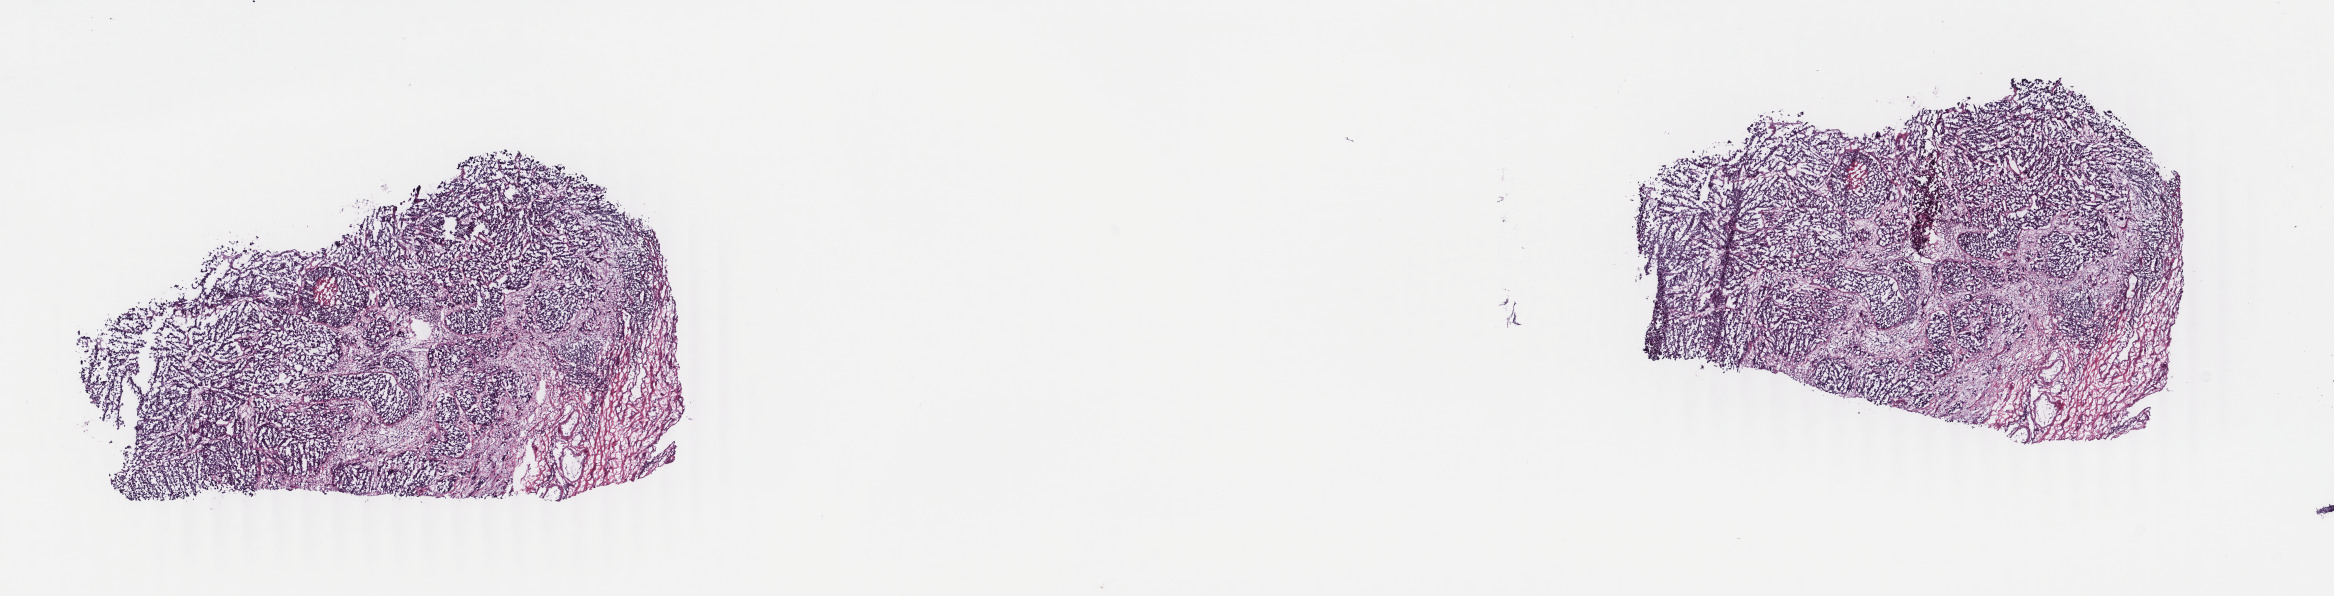
Digitized H&E-stained tissue section (whole slide), shown as a low-resolution overview of the whole scanned area (about 18.6 x 4.7 mm, acquisition: 40x scan). Frozen section. Bladder, primary tumour sample. Patient: female, age at initial diagnosis 67 years. Histologic grade: high grade. Pathologist review of this section (percent, as recorded): tumour cells 85%, tumour nuclei 85%, normal cells 0%, stromal cells 14%, necrosis 1%. Infiltration values recorded for this section: lymphocyte infiltration 2%, monocyte infiltration 1%, neutrophil infiltration 1%.
Diagnosis: Transitional cell carcinoma. AJCC pathologic stage: IV (6th edition).